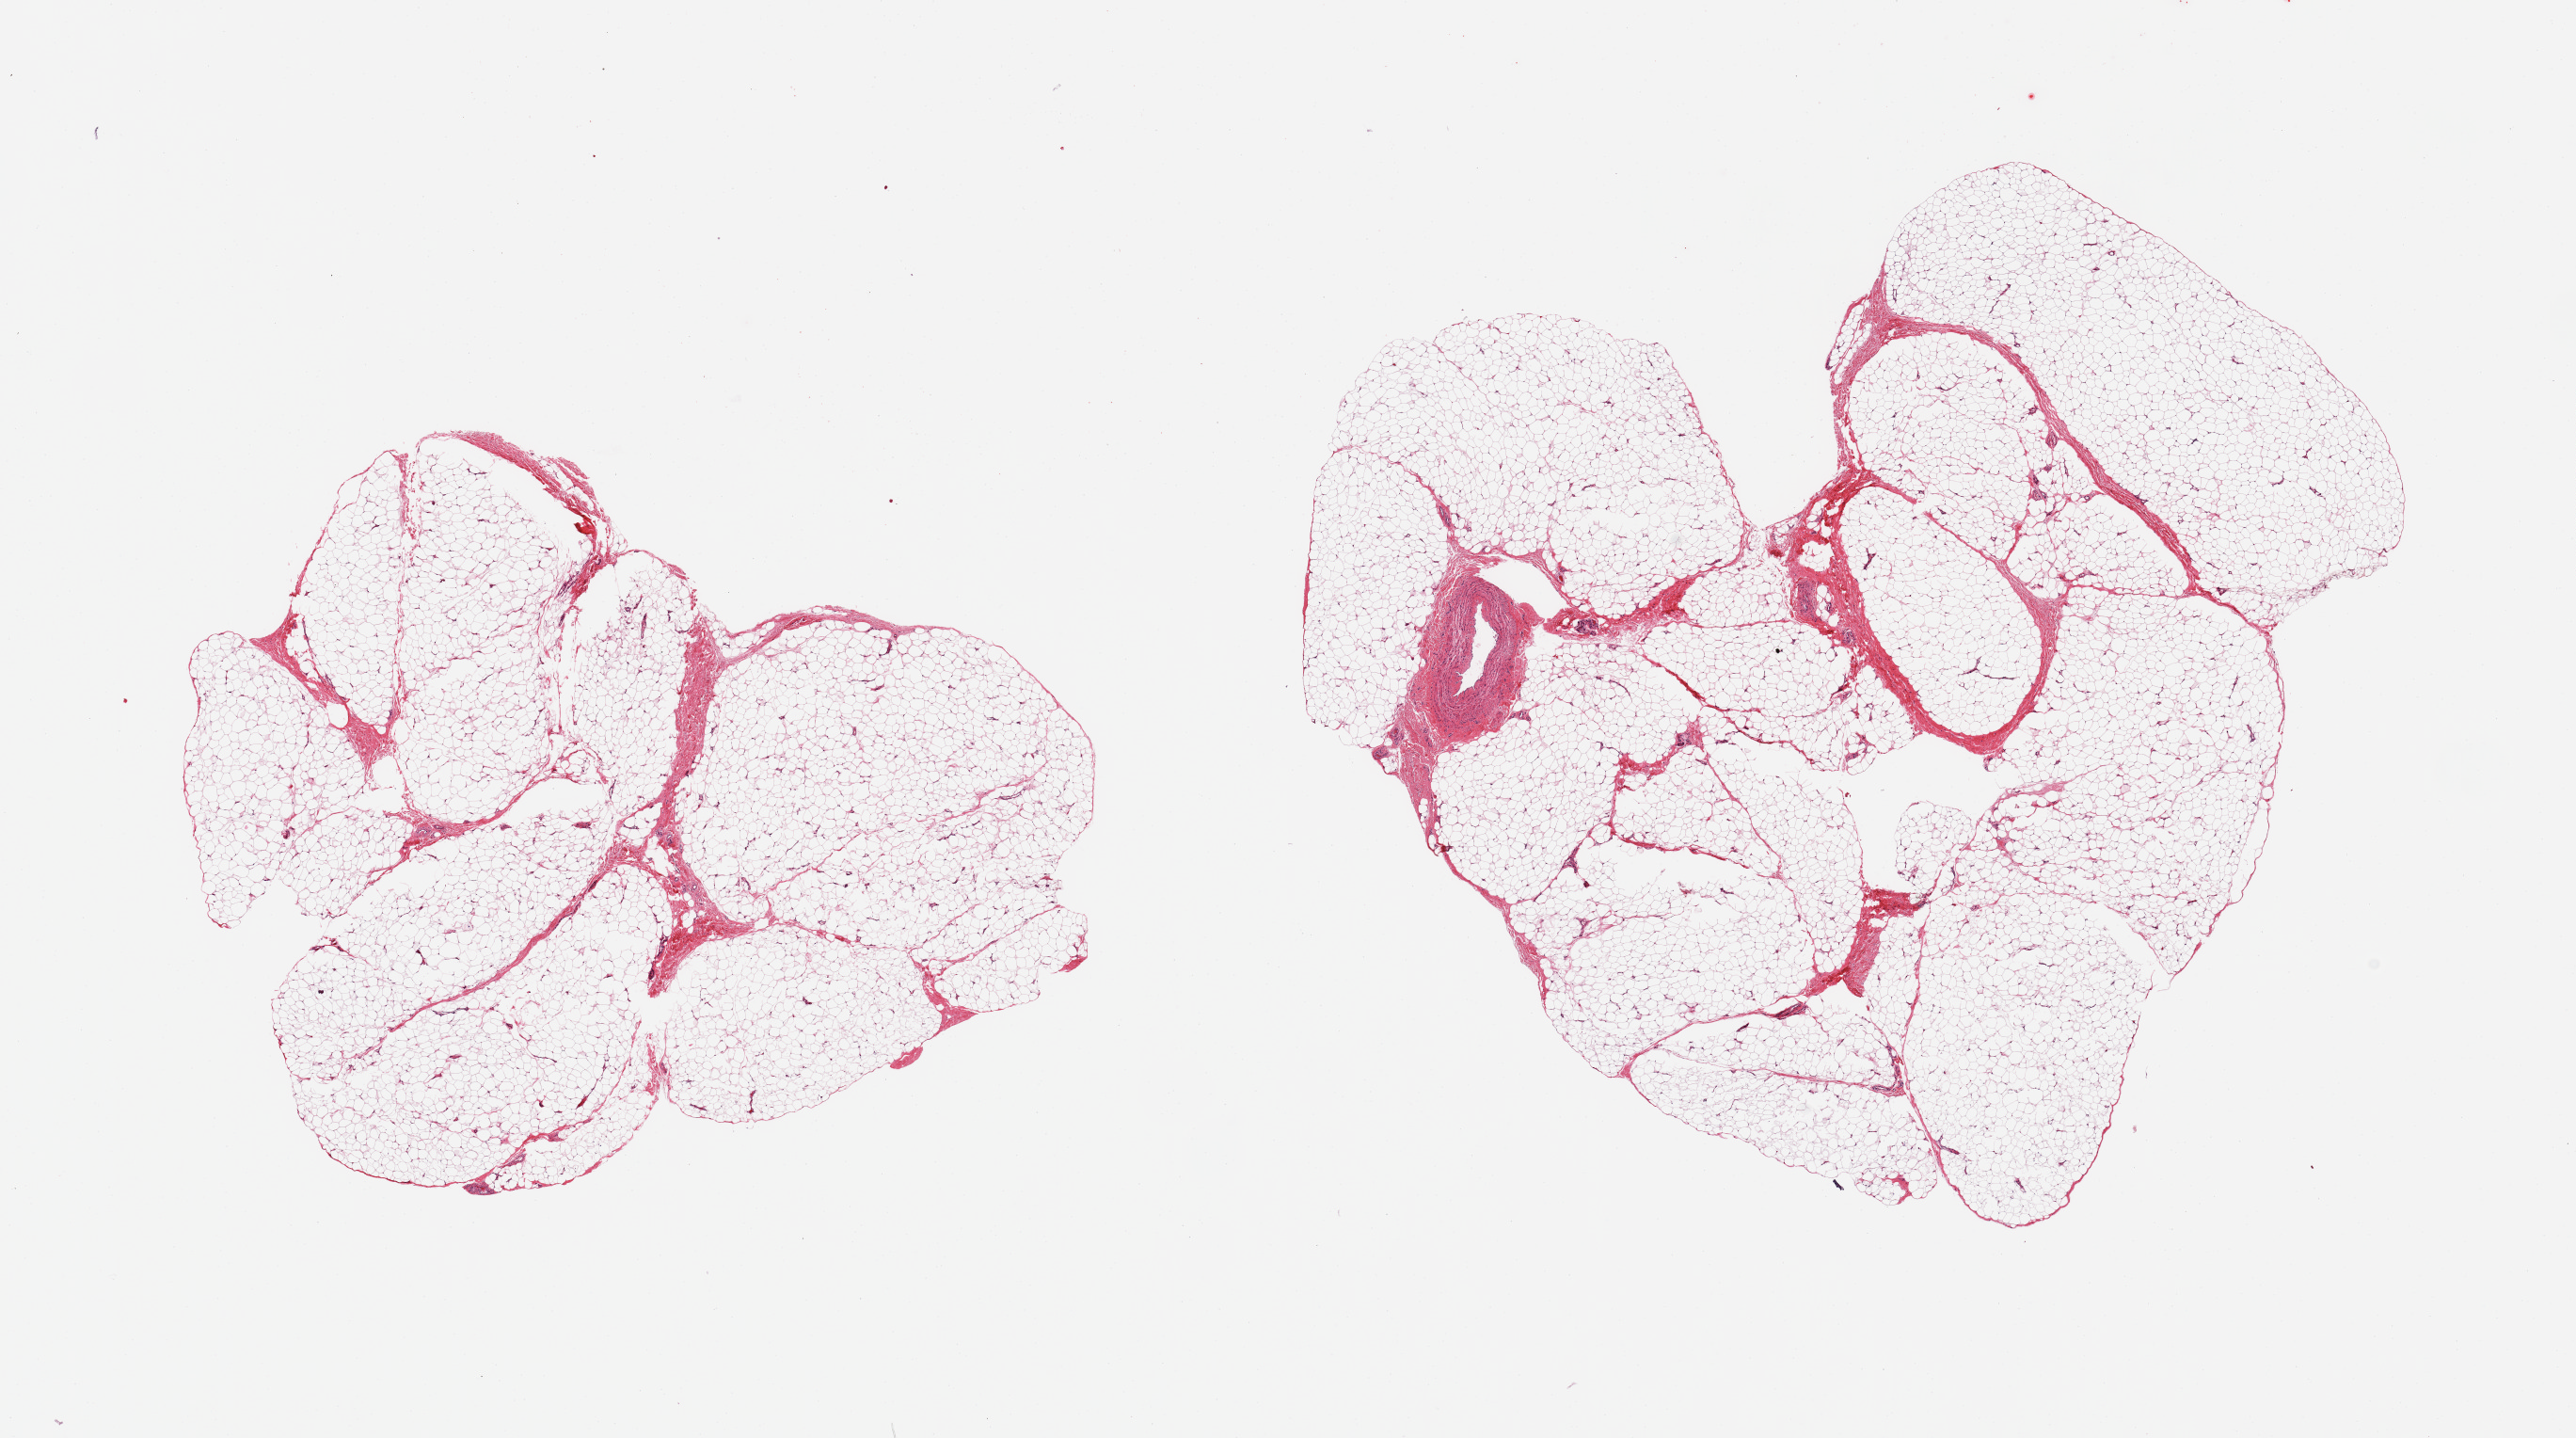
Haematoxylin and eosin whole-slide image — a low-resolution overview of the entire scanned area, about 21.7 x 12.1 mm (from a 20x scan); PAXgene-fixed paraffin-embedded (PFPE) section; sampled site (target tissue): adipose tissue; donor tissue sample. Female donor.
* review note (as recorded): 2 pieces; mature adipose tissue with small portion of fibrous tissue/vessel